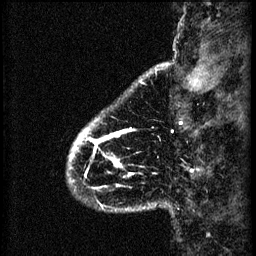
Breast MRI (dynamic contrast-enhanced), one sagittal slice. Slice 8 of 60 in the series (ordered by position). 3 images stored at this slice position (order not interpretable as contrast timing). 1.5 T. TE 4.2 ms, TR 8.2 ms. 2.2 mm slice thickness. 256 × 256 image matrix, field of view 180 × 180 mm. Female patient, age 41 years.
Annotated regions visible in this slice (semi-automatic segmentation, software-assisted and operator-edited):
- analysis volume of interest (the breast-tissue region the enhancement analysis was run in; not a lesion): box from (x=68, y=118) to (x=157, y=207) px
- tumour enhancement mask (voxels above the 70 % enhancement threshold inside the analysis volume of interest): (x=70, y=128)–(x=134, y=189)